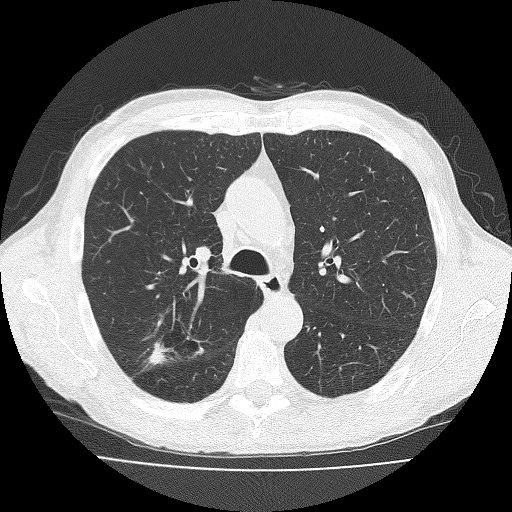
Axial slice from a low-dose chest CT screening exam; third annual screen; lung window (W 1500 / L -600 HU); 2 mm slice thickness; 512 × 512 image matrix, field of view 350 × 350 mm. Male, age 73 years at enrolment. Current smoker at enrolment.
- Expert reader's lesion annotation, bounding box (x1, y1, x2, y2) in pixels: (139, 324, 192, 378).
- Screening reader's record for this exam (one nodule recorded; not confirmed to be the boxed lesion): non-calcified nodule or mass ≥4 mm, right upper lobe, 11 × 10 mm, spiculated (stellate) margins, soft tissue attenuation, pre-existing on the prior screen: no.
- Official screen result: positive, other.
- Lung cancer was diagnosed 38 days after this screen: adenosquamous carcinoma, right upper lobe, well differentiated (G1), stage IA (AJCC 6th edition), 20 mm at pathology.